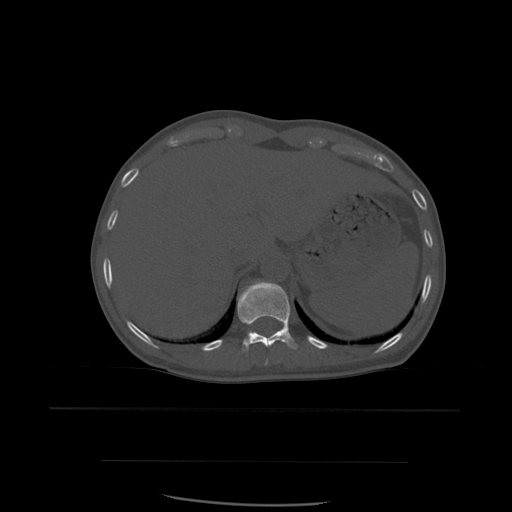
CT including the spine, one axial slice; slice 294 of 574 in the series (ordered by position); bone window (W 1800 / L 400 HU); 1.25 mm slice thickness; 512 × 512 image matrix. Patient age 48 years. From the clinical record (not read from this slice): primary cancer: lung.
Structures marked on this image (semi-automatic segmentation, software-assisted and operator-edited):
- T10 vertebra: box from (x=265, y=359) to (x=269, y=366) px
- T11 vertebra: (x=238, y=281)–(x=298, y=353)